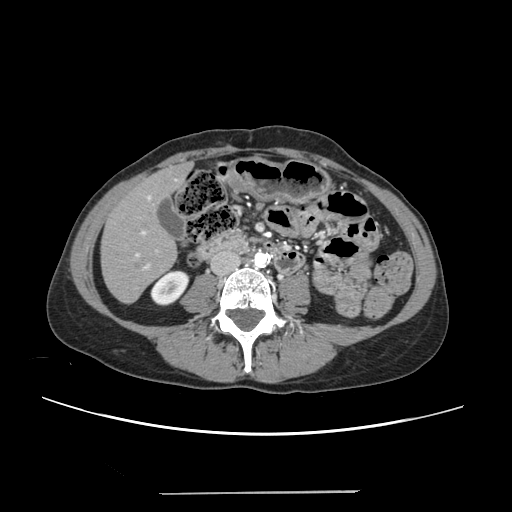
Contrast-enhanced abdominal CT, one axial slice; slice 67 of 240 in the series (ordered by position); 120 kVp; intravenous contrast given; soft-tissue window (W 400 / L 40 HU); 1.25 mm slice thickness; 512 × 512 image matrix, field of view 371 × 371 mm. Female patient, age 60 years. Case-level facts recorded for this patient, not image findings: diagnosis: colorectal cancer liver metastases, imaged before liver resection; multiple liver metastases: no; largest metastasis: 1.5 cm; disease in both lobes: no.
Annotated regions visible in this slice (manually delineated by an expert):
- liver: box from (x=102, y=166) to (x=187, y=302) px
- planned liver remnant (the part of the liver to remain after resection): (x=102, y=171)–(x=177, y=302)
- portal vein (with intrahepatic branches): (x=135, y=196)–(x=158, y=269)